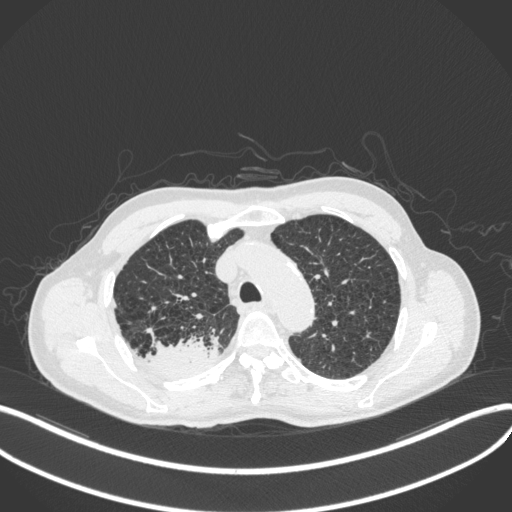
Chest CT, one axial slice; slice 335 of 423 in the series (ordered by position); reconstruction kernel B31f; 120 kVp; lung window (W 1500 / L -600 HU); 512 × 512 image matrix, field of view 400 × 400 mm. Patient: male, 79 years. From the clinical record (not read from this slice): clinical TNM (as recorded): T3 N0 M0.
Annotated regions visible in this slice (bounding box drawn by a radiologist):
- lung tumour (recorded histology: adenocarcinoma): bounding box [x1, y1, x2, y2] px = [142, 336, 219, 380]